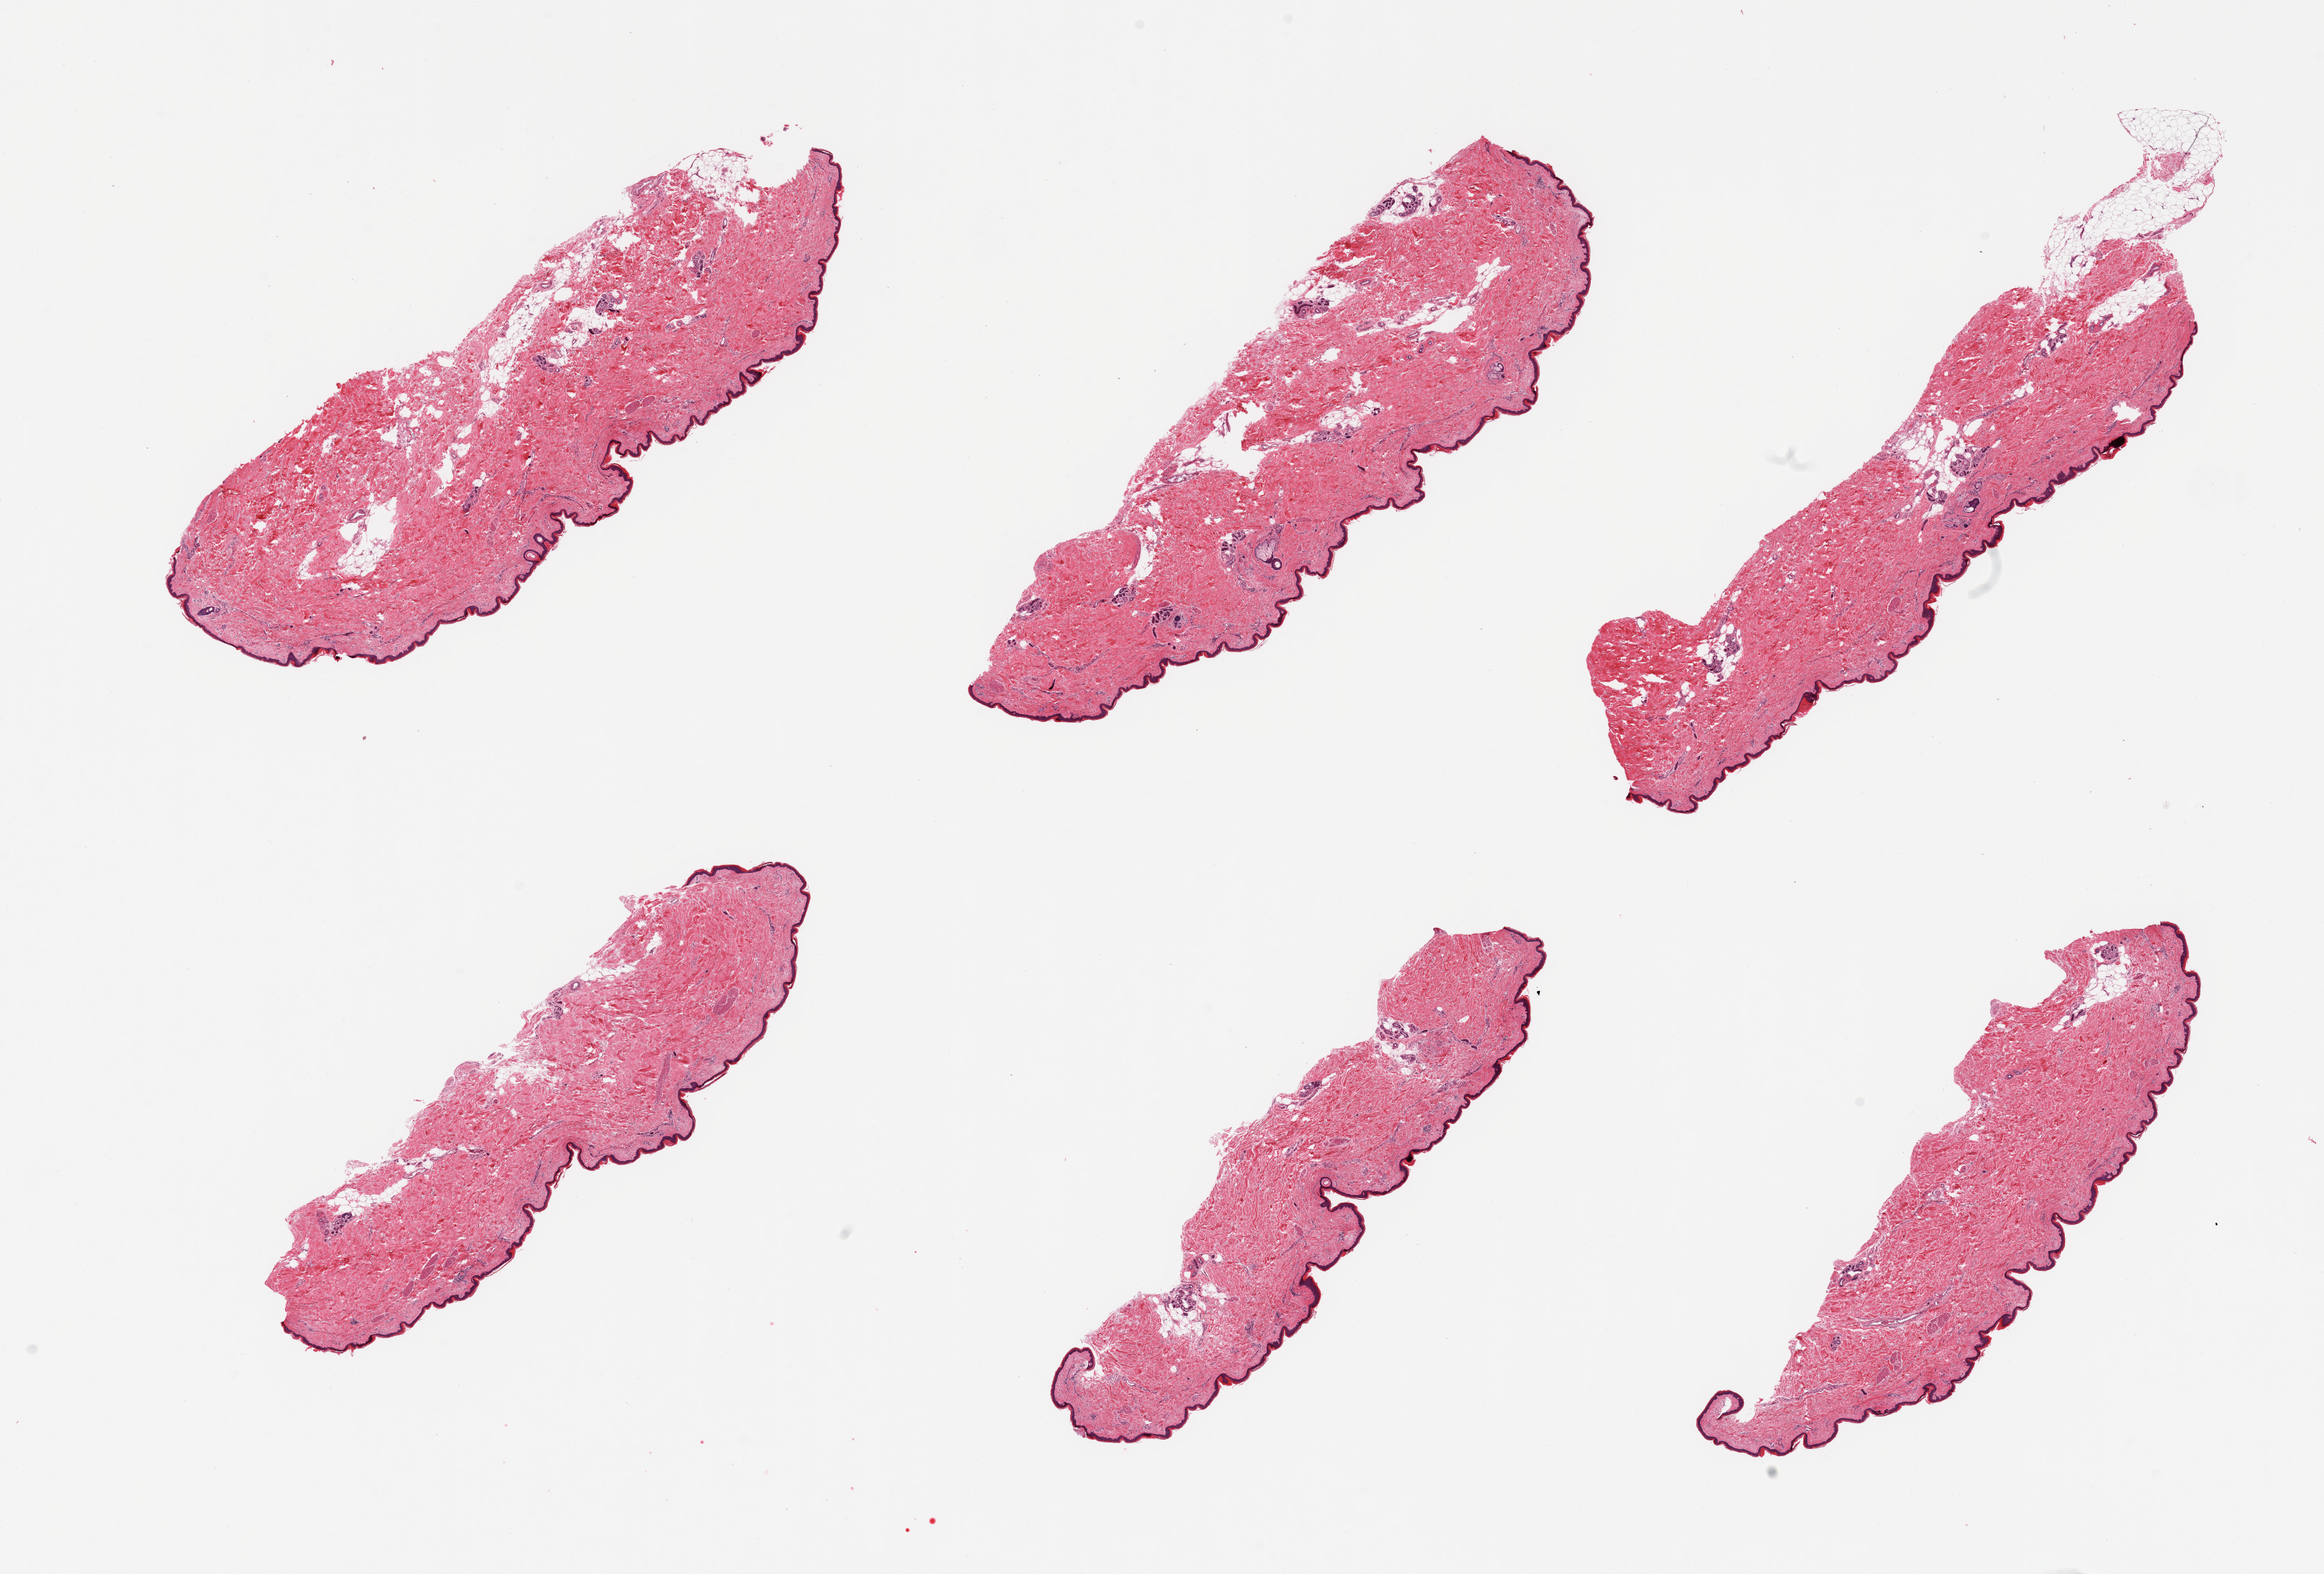
H&E whole-slide image, low-resolution overview of the scanned area, about 25.6 x 17.3 mm; PAXgene-fixed paraffin-embedded (PFPE) section; sampled site (target tissue): skin of lower leg; donor tissue sample. Male donor.
Pathologist's review note for this sample: 6 pieces, minimal dermal fat, squamous epithelium is ~30 microns.